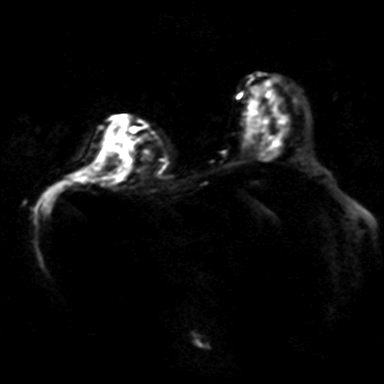
Breast MRI, one axial slice. Position 22 of 40 along the scan axis. Diffusion-weighted series; image 2 of 4 stored at this slice position (different b-values; order by instance number). 3 T. 4.2 mm slice thickness. 384 × 384 image matrix, field of view 320 × 320 mm. Female patient.
Outlined on this slice (expert manual segmentation):
- tumour on diffusion-weighted imaging: bounding box (x1, y1, x2, y2) in pixels: (109, 144, 114, 148)